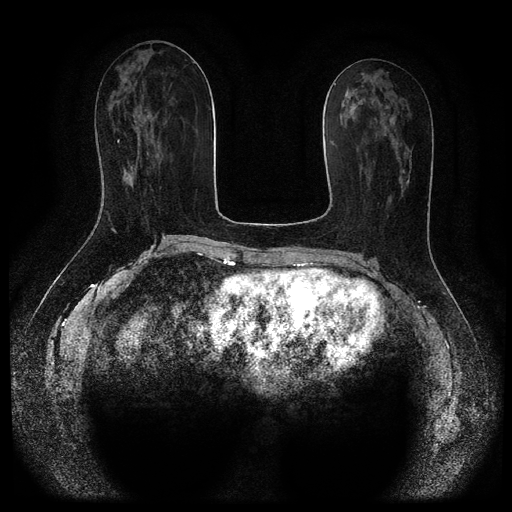
Breast MRI (dynamic contrast-enhanced, multi-phase), one axial slice; slice 44 of 116 in the series (ordered by position); dynamic contrast-enhanced series, time point 2 of 5 at this slice position (early post-contrast); 1.5 T; TE 2.7 ms, TR 5.4 ms; 2 mm slice thickness; 512 × 512 image matrix, field of view 340 × 340 mm. Female patient, age 47 years.
Structures marked on this image (semi-automatic segmentation, software-assisted and operator-edited):
- breast lesion (labelled benign in the annotation): bounding box (x1, y1, x2, y2) in pixels: (389, 115, 396, 125)